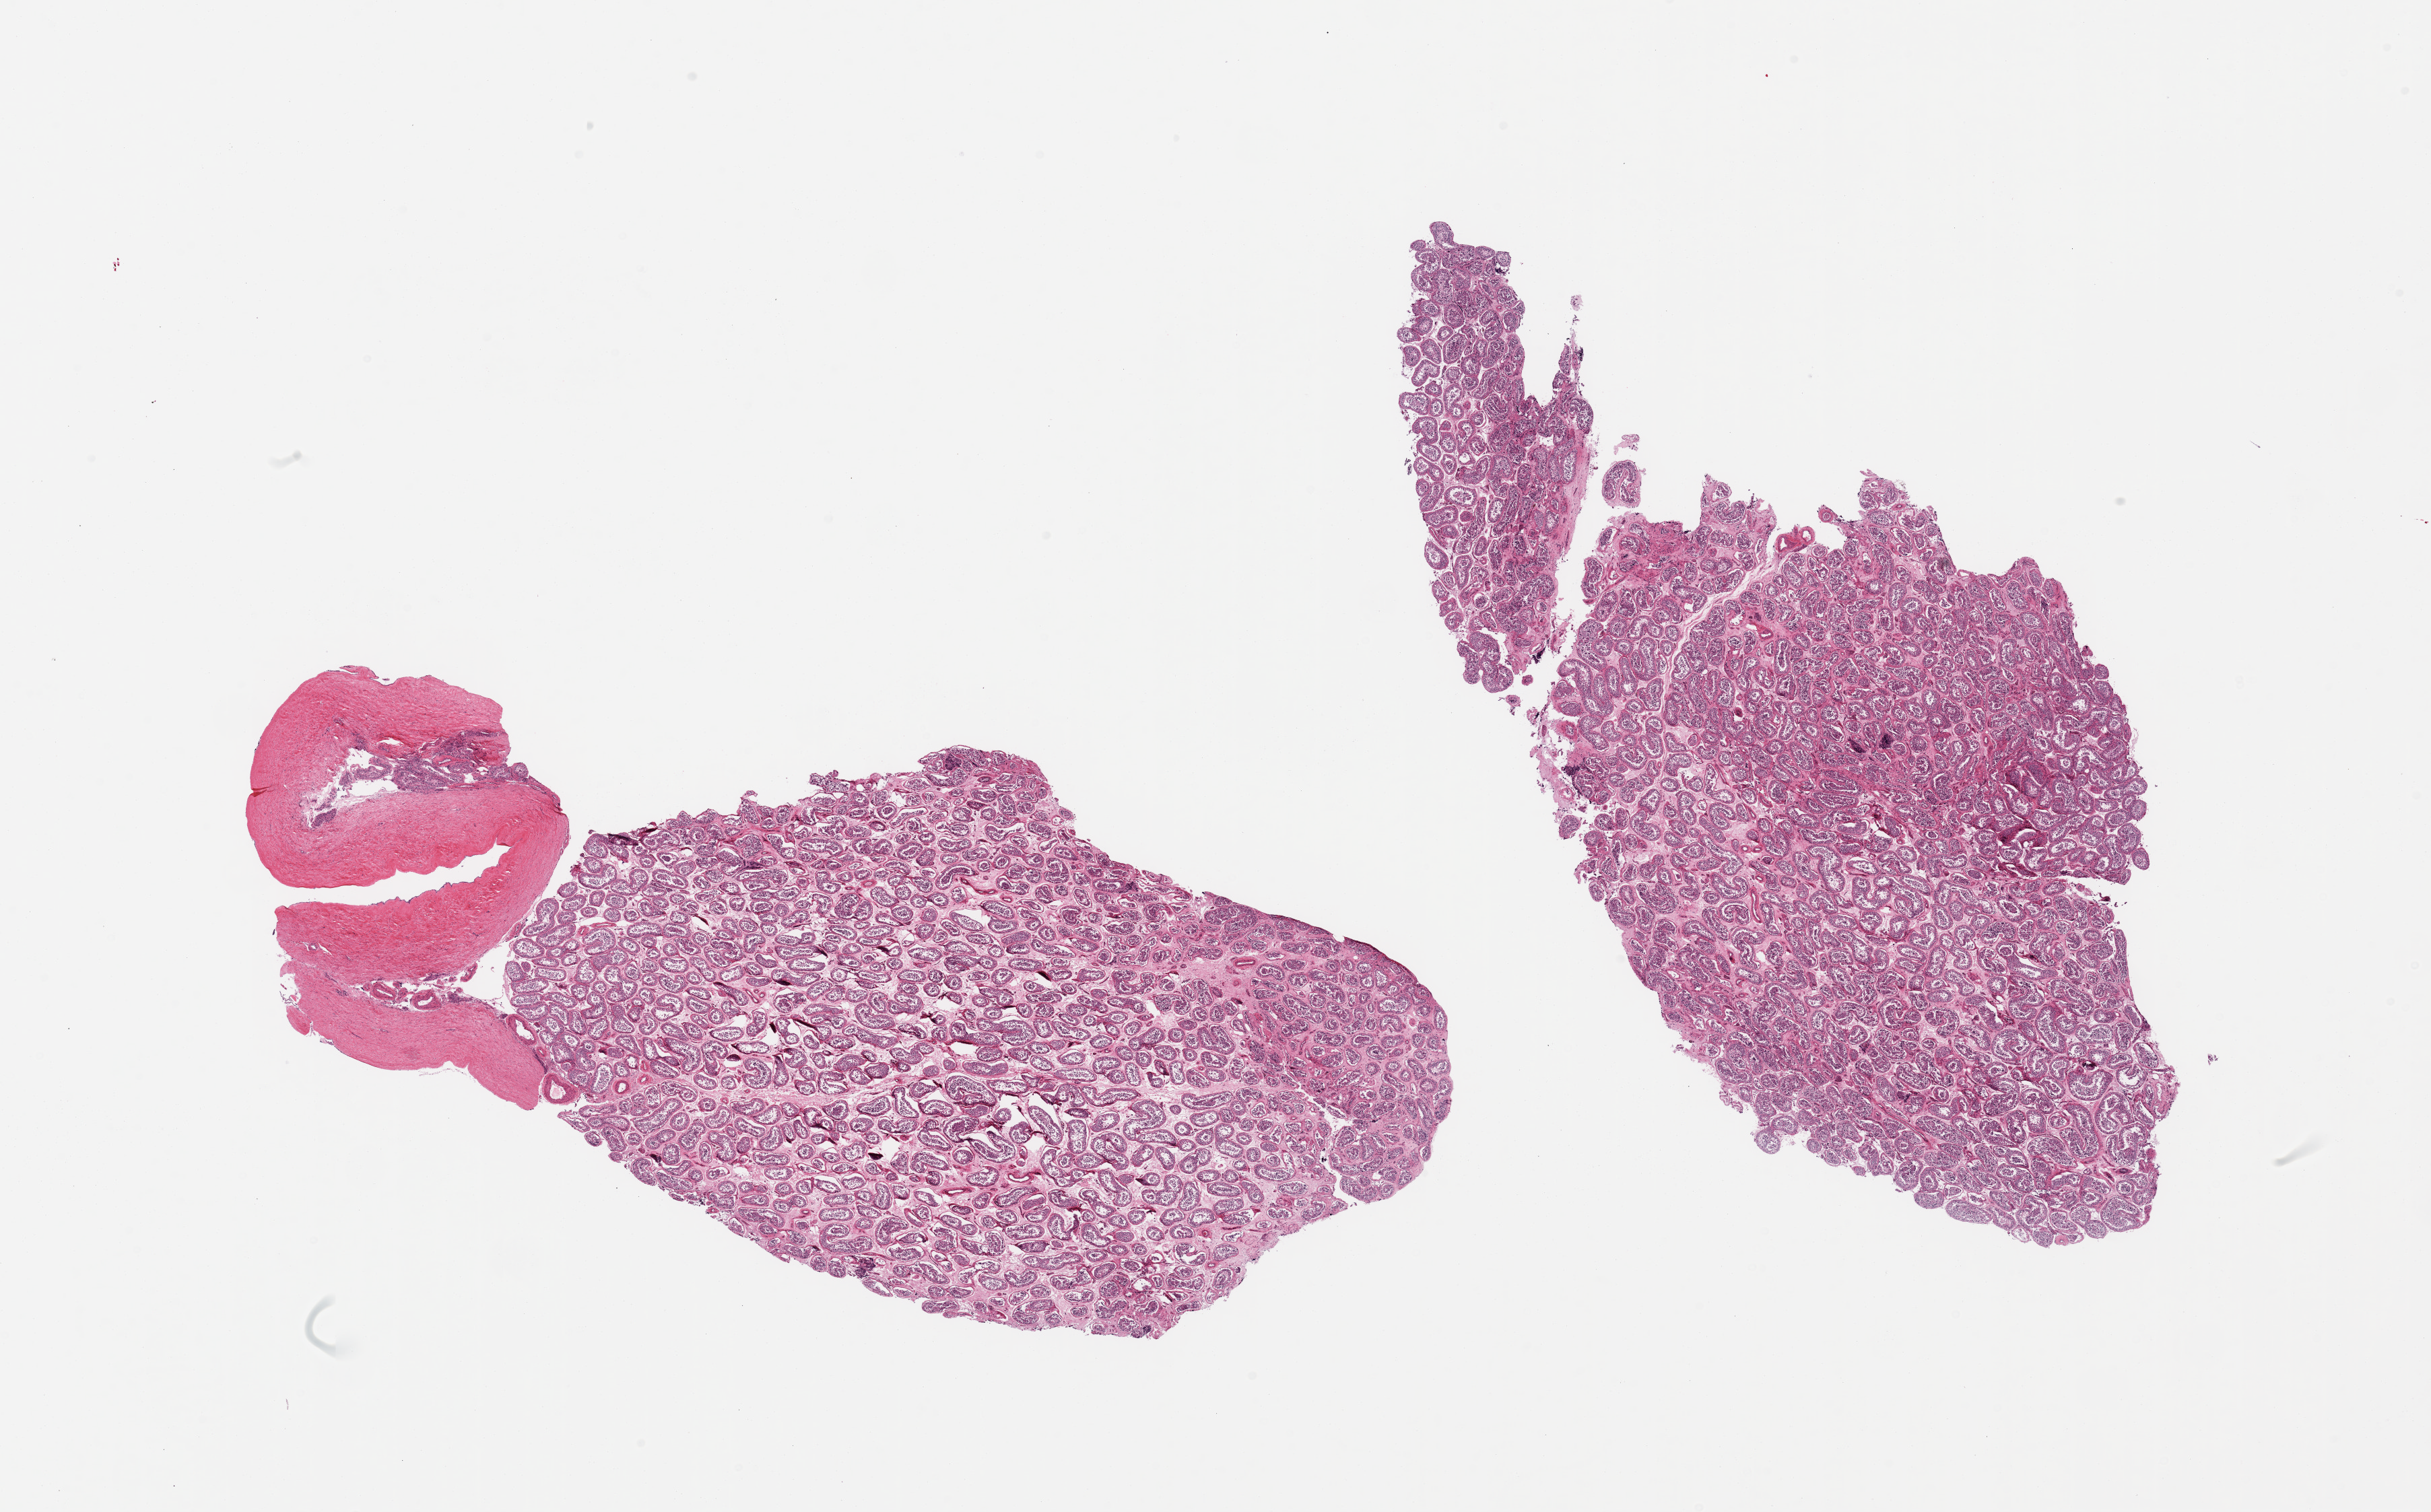
Whole-slide image, H&E stain — a low-resolution overview of the entire scanned area, about 28.5 x 17.8 mm, PAXgene-fixed paraffin-embedded (PFPE) section, sampled site (target tissue): testis, tissue donor sample. Donor sex: male.
Review note (as recorded): 2 pieces, spermatogenesis present.